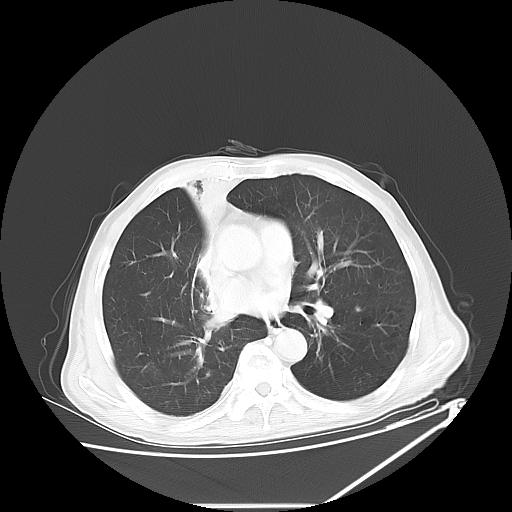
Chest CT, one axial slice; position 33 of 60 along the scan axis; reconstruction kernel LUNG; lung window (W 1500 / L -600 HU); 5 mm slice thickness; 512 × 512 image matrix, field of view 410 × 410 mm. Patient: male, 73 years. Case-level facts recorded for this patient, not image findings: clinical TNM (as recorded): T2a N1 M0.
Annotated regions visible in this slice (rectangle marked by the reading radiologist):
- lung tumour (recorded histology: squamous cell carcinoma): bounding box [x1, y1, x2, y2] px = [178, 177, 233, 249]